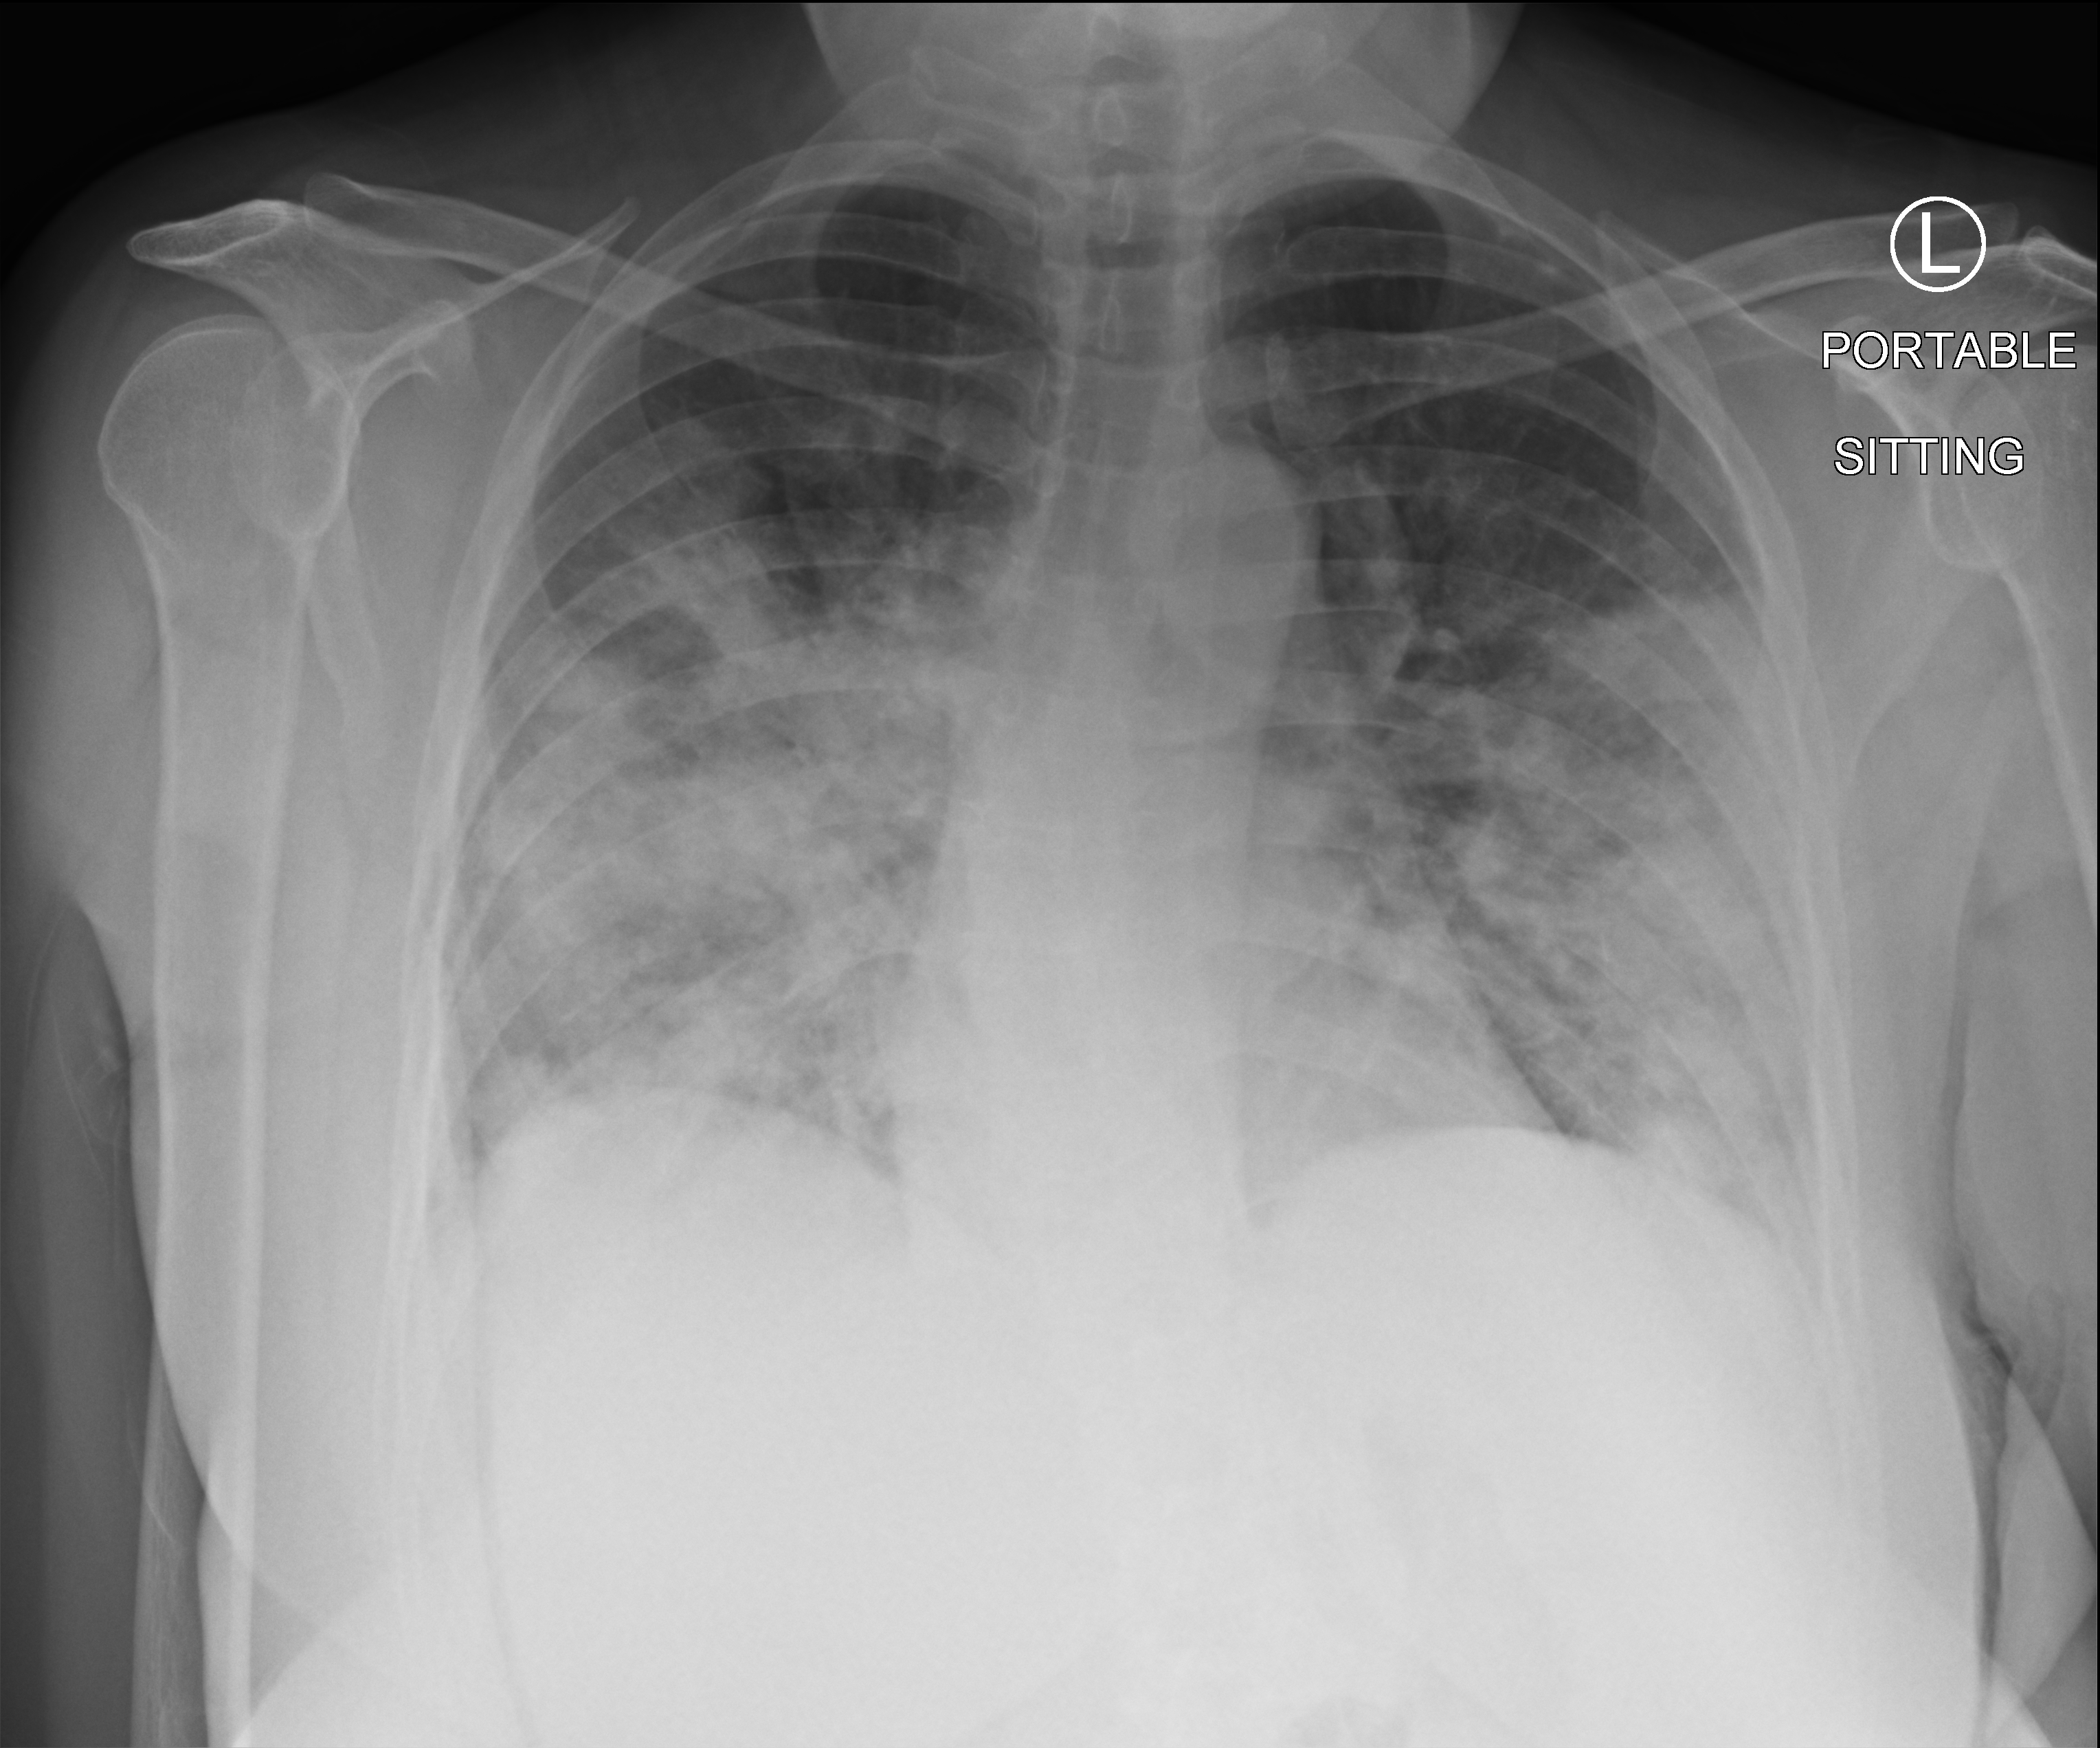
Portable chest radiograph; anteroposterior (AP) projection. Female patient hospitalised with COVID-19, age 18–59 years.
From the hospital-stay record, not from the radiograph (when in the stay this image was taken is not recorded): other chronic lung disease (admission record): no; mechanically ventilated during this hospital stay: no; diabetes (admission record): no.